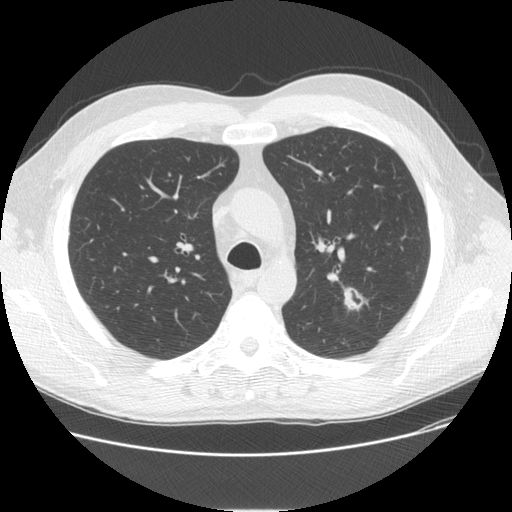
Chest CT (low-dose screening protocol), one axial image. Third screening round (two years after baseline). Lung window (W 1500 / L -600 HU). 2.5 mm slice thickness. Slice 40 of 150 in the series. 512 × 512 image matrix, field of view 370 × 370 mm. Male participant, aged 57 years at enrolment. Current smoker at enrolment.
Expert reader's lesion annotation, bounding box <323,282,373,322> (left, top, right, bottom; pixels). The exam's reader record, not a measurement of the box and not confirmed to be the same lesion: non-calcified nodule or mass ≥4 mm, left upper lobe, 17 × 13 mm, spiculated (stellate) margins, mixed attenuation, pre-existing on the prior screen: yes; interval growth: yes. Official screen result: positive, other.